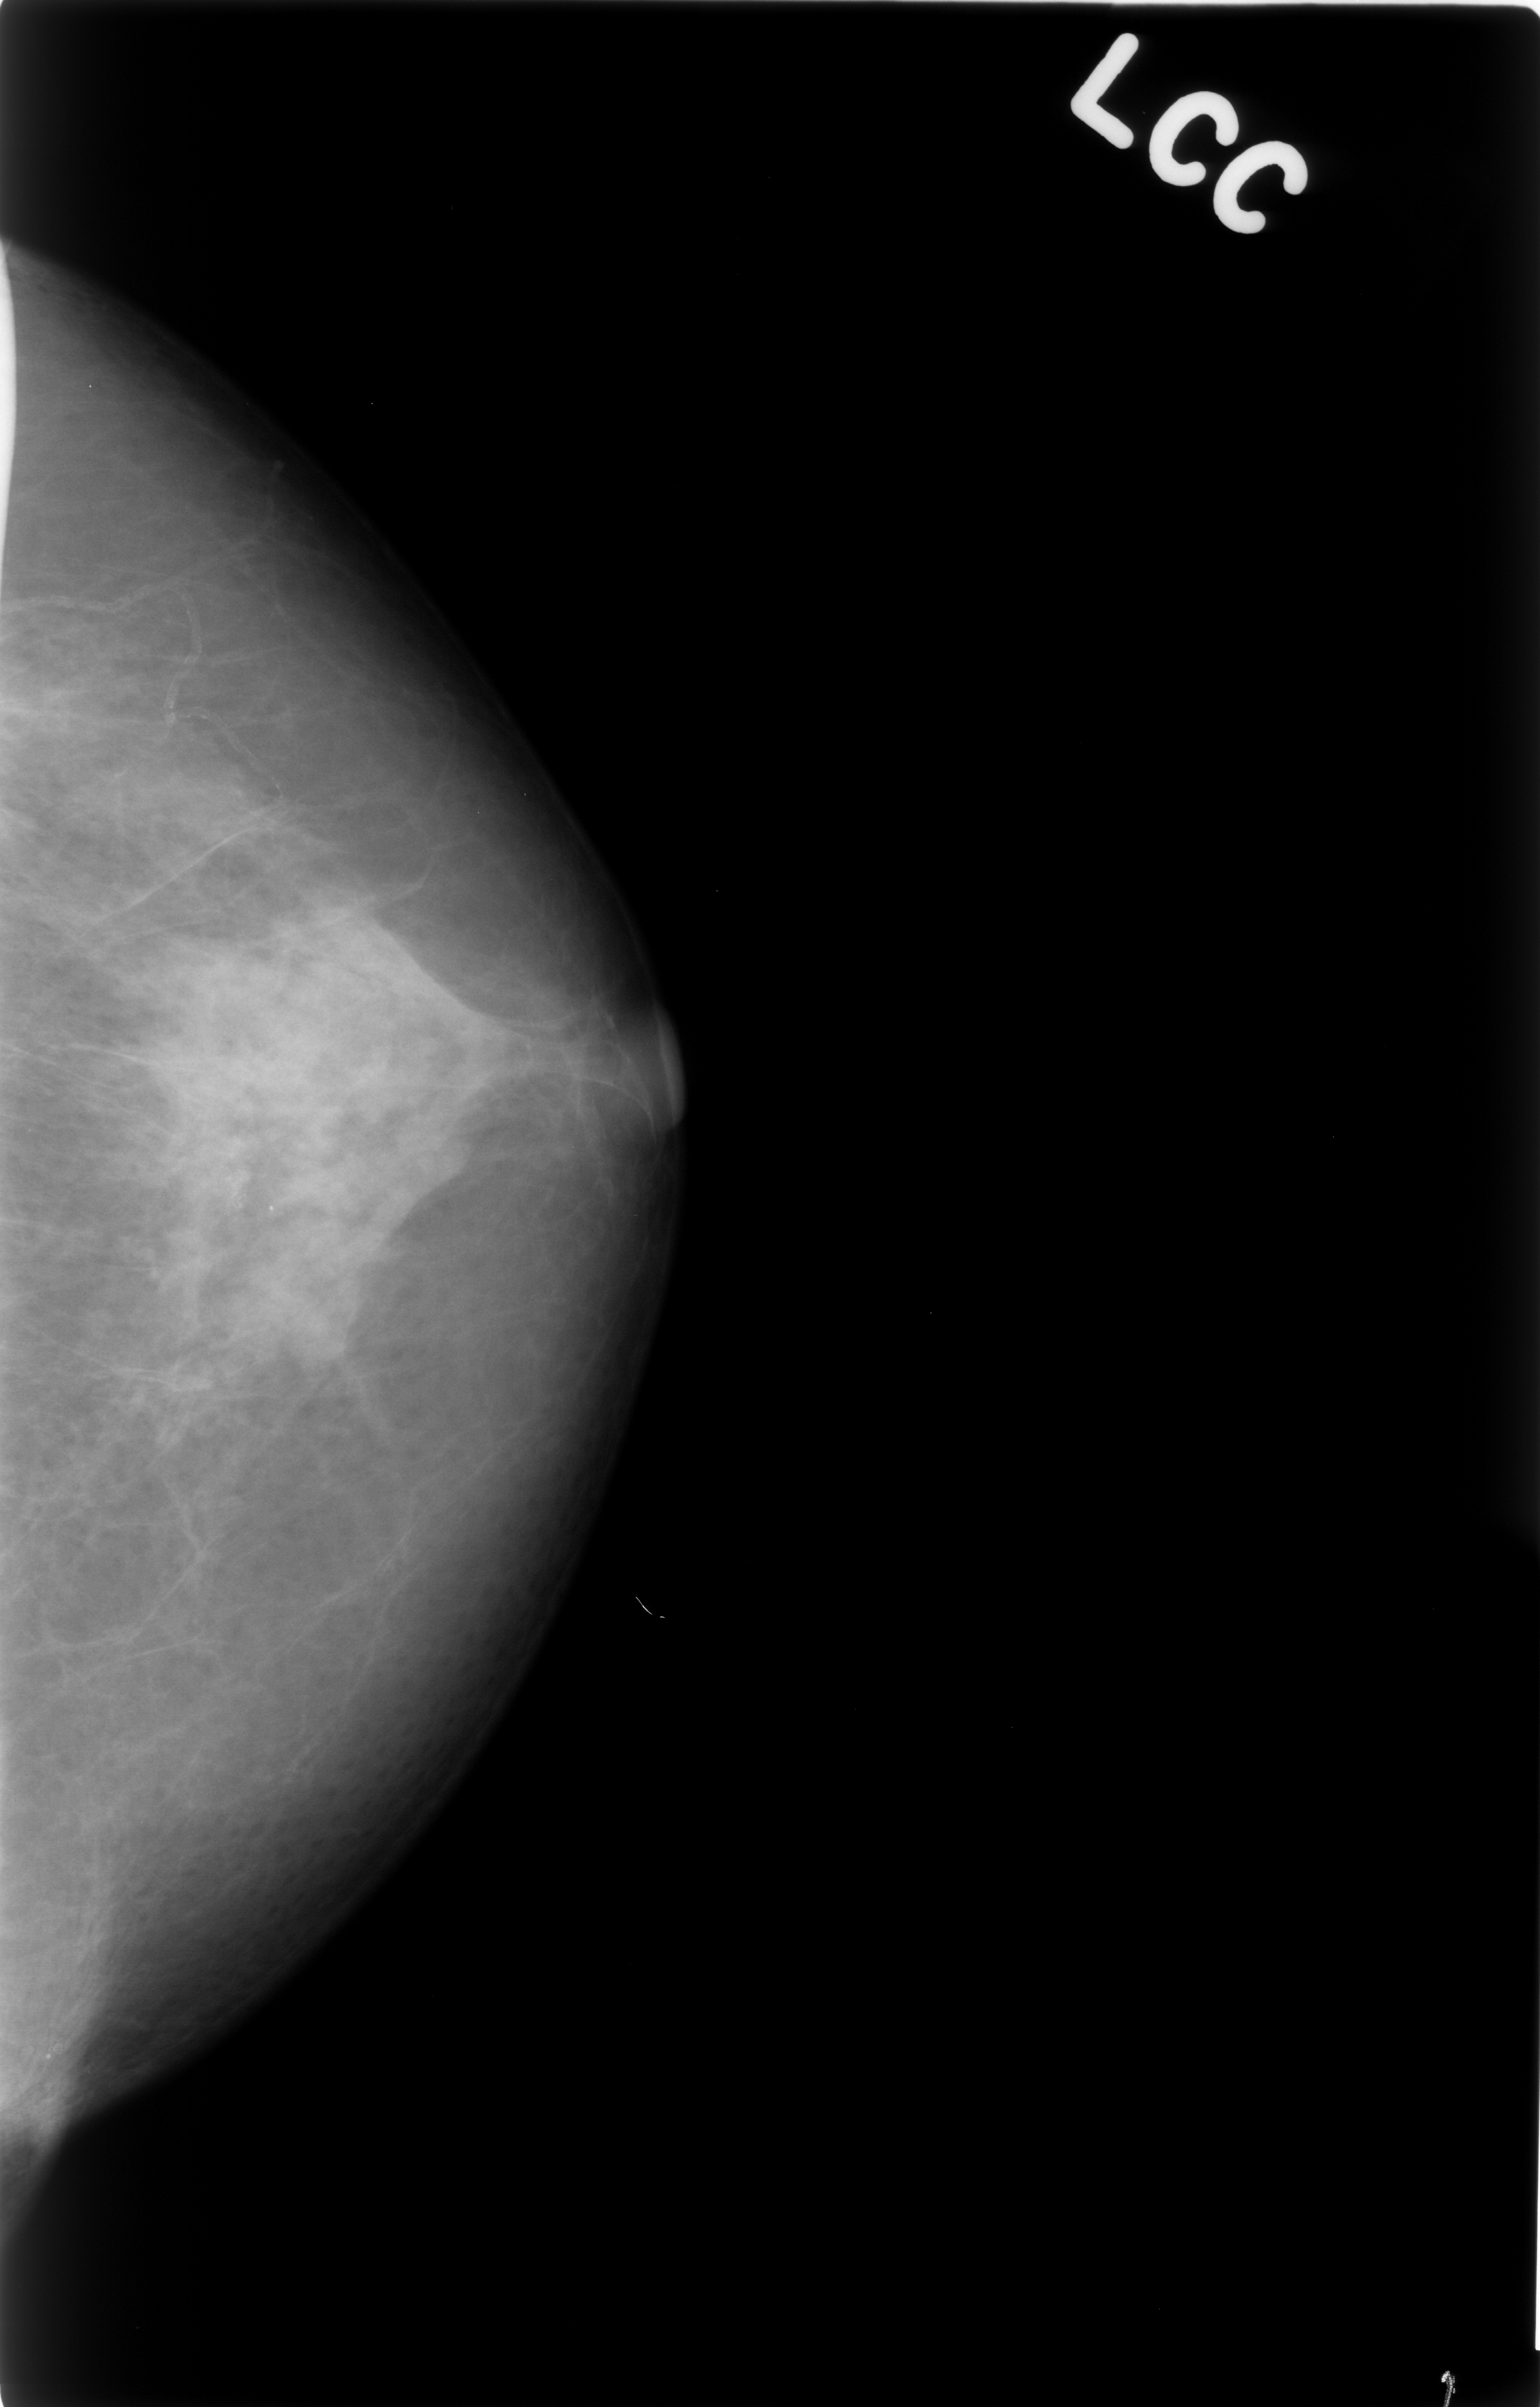
Mammogram (digitized film); left breast; craniocaudal (CC) view; 1540 × 2407 image matrix.
Expert-marked regions of interest on this film, with their recorded descriptors:
- calcifications, morphology amorphous, distribution clustered; BI-RADS assessment category 4; subtlety rating 2 on a 1 (subtle) to 5 (obvious) scale; pathology result (as recorded, not read from the image): benign: bounding box <109,1199,262,1352> (left, top, right, bottom; pixels)